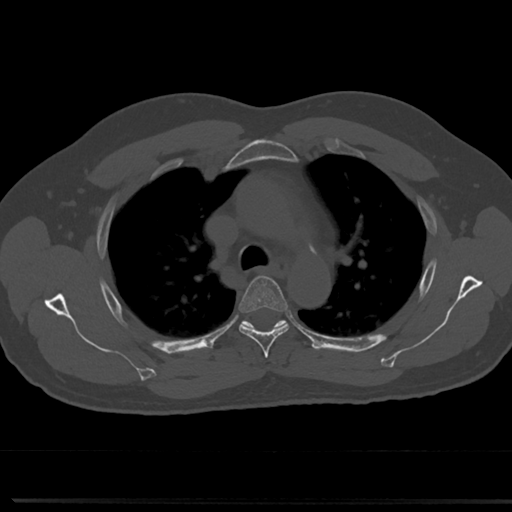
CT including the spine, one axial slice. Slice 534 of 817 in the series (ordered by position). 120 kVp. Bone window (W 1800 / L 400 HU). 0.5 mm slice thickness. 512 × 512 image matrix. Male patient, age 61 years. From the clinical record (not read from this slice): primary cancer: prostate.
Outlined on this slice (semi-automatic segmentation, software-assisted and operator-edited):
- T4 vertebra: bounding box [x1, y1, x2, y2] px = [238, 275, 290, 355]
- T5 vertebra: [245, 321, 283, 326]